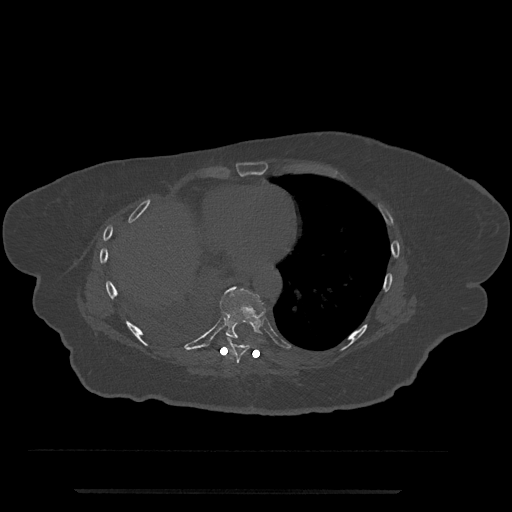
CT including the spine, one axial slice. Position 365 of 797 along the scan axis. Bone window (W 1800 / L 400 HU). 512 × 512 image matrix, field of view 440 × 440 mm. Female patient, age 51 years. From the clinical record (not read from this slice): primary cancer: neuro; vertebrae with lytic lesions (as recorded): T8.
Outlined on this slice (semi-automatically segmented with operator editing):
- T8 vertebra: box from (x=227, y=338) to (x=249, y=364) px
- T9 vertebra: (x=217, y=286)–(x=266, y=344)